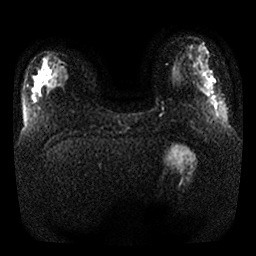
Breast MRI, one axial slice. Position 6 of 32 along the scan axis. Diffusion-weighted series; image 2 of 4 stored at this slice position (different b-values; order by instance number). 1.5 T. 256 × 256 image matrix. Female patient.
Outlined on this slice (manually delineated by an expert):
- tumour on diffusion-weighted imaging: box from (x=54, y=67) to (x=67, y=83) px